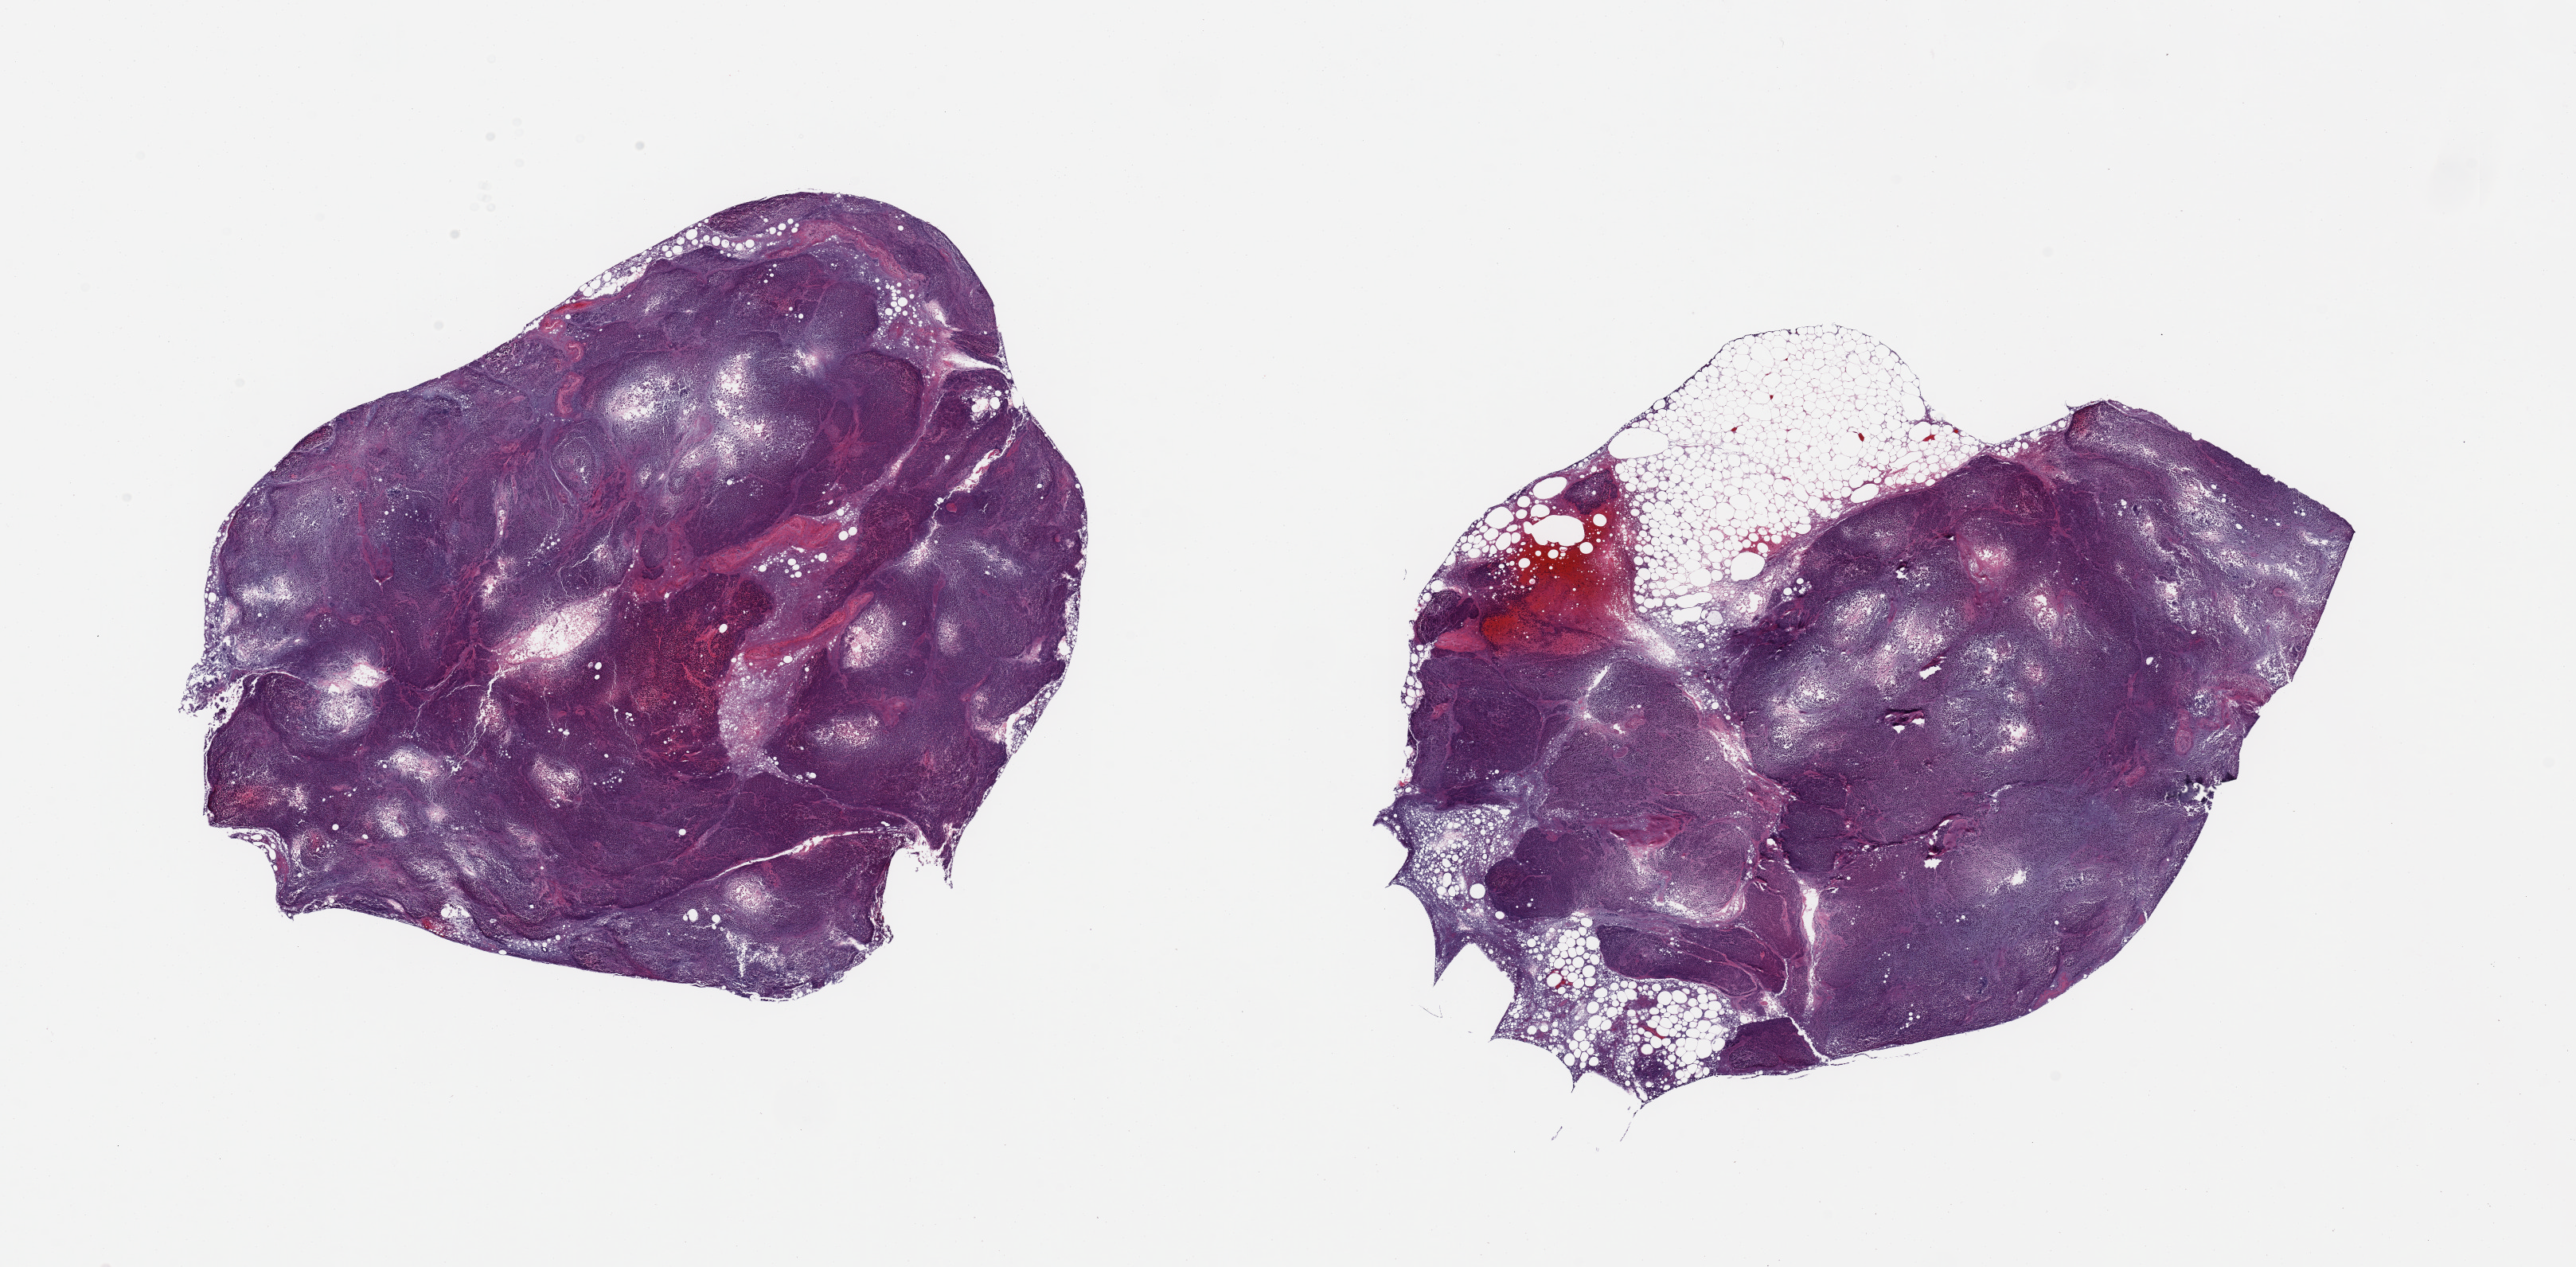
Haematoxylin and eosin whole-slide image — low-resolution overview of the scanned area, about 25.6 x 12.6 mm (from a 20x scan); PAXgene-fixed, paraffin-embedded tissue; sampled site (target tissue): pancreas; tissue donor sample. Donor: male.
Reviewer comment on this tissue sample: 2 pieces; severe autolysis, one piece contain ~15% external fat.